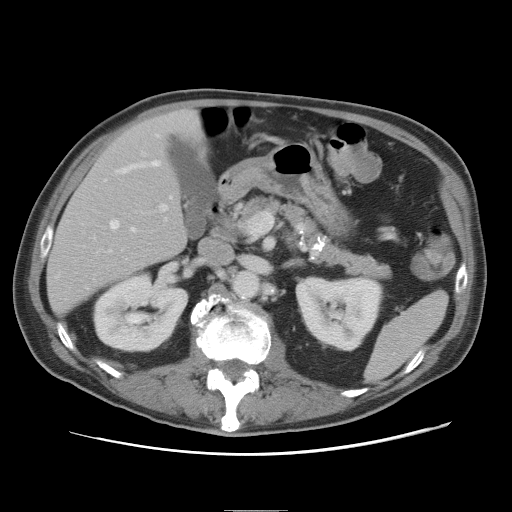
Contrast-enhanced abdominal CT, one axial slice. Position 36 of 89 along the scan axis. 120 kVp. Intravenous contrast given. Soft-tissue window (W 400 / L 40 HU). 5 mm slice thickness. 512 × 512 image matrix, field of view 375 × 375 mm. Male patient, age 69 years. From the clinical record (not read from this slice): diagnosis: colorectal cancer liver metastases, imaged before liver resection; multiple liver metastases: no; largest metastasis: 8.5 cm; disease in both lobes: no.
Annotated regions visible in this slice (expert manual segmentation):
- hepatic veins: box from (x=111, y=134) to (x=172, y=231) px
- liver: (x=47, y=111)–(x=206, y=313)
- planned liver remnant (the part of the liver to remain after resection): (x=47, y=111)–(x=207, y=314)
- portal vein (with intrahepatic branches): (x=110, y=204)–(x=169, y=252)